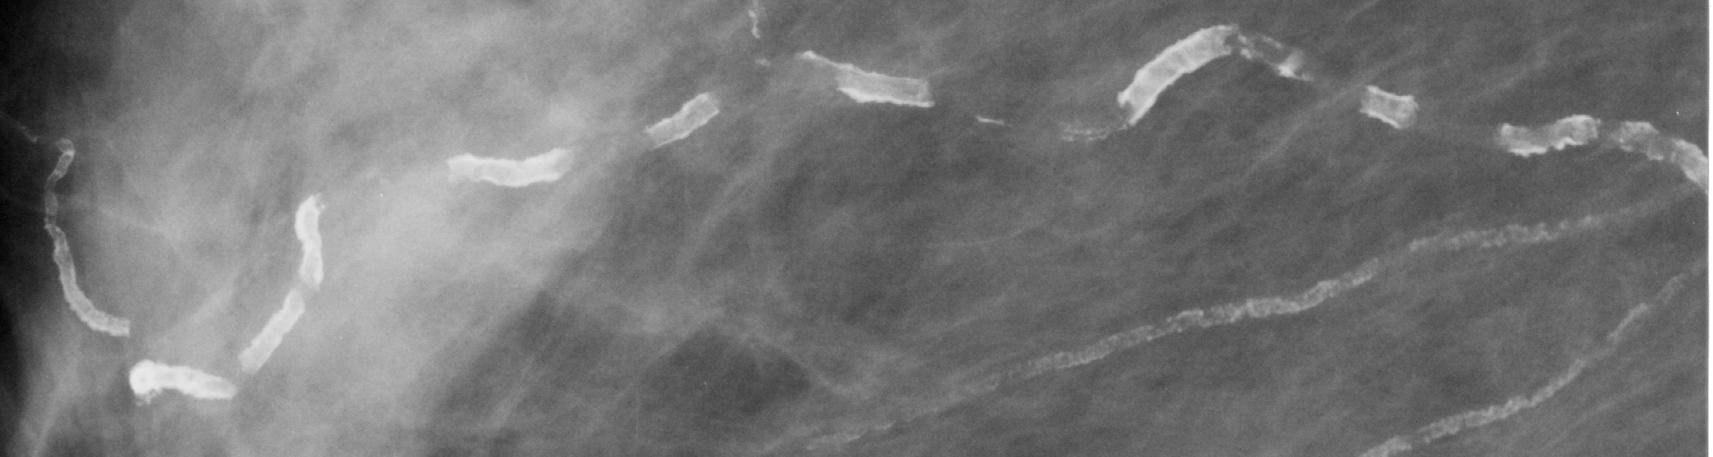
Region of interest cut from a scanned film mammogram (one marked finding), right breast, MLO view.
Marked abnormality: calcifications, morphology vascular; BI-RADS assessment category 2; benign without callback (not worked up further).